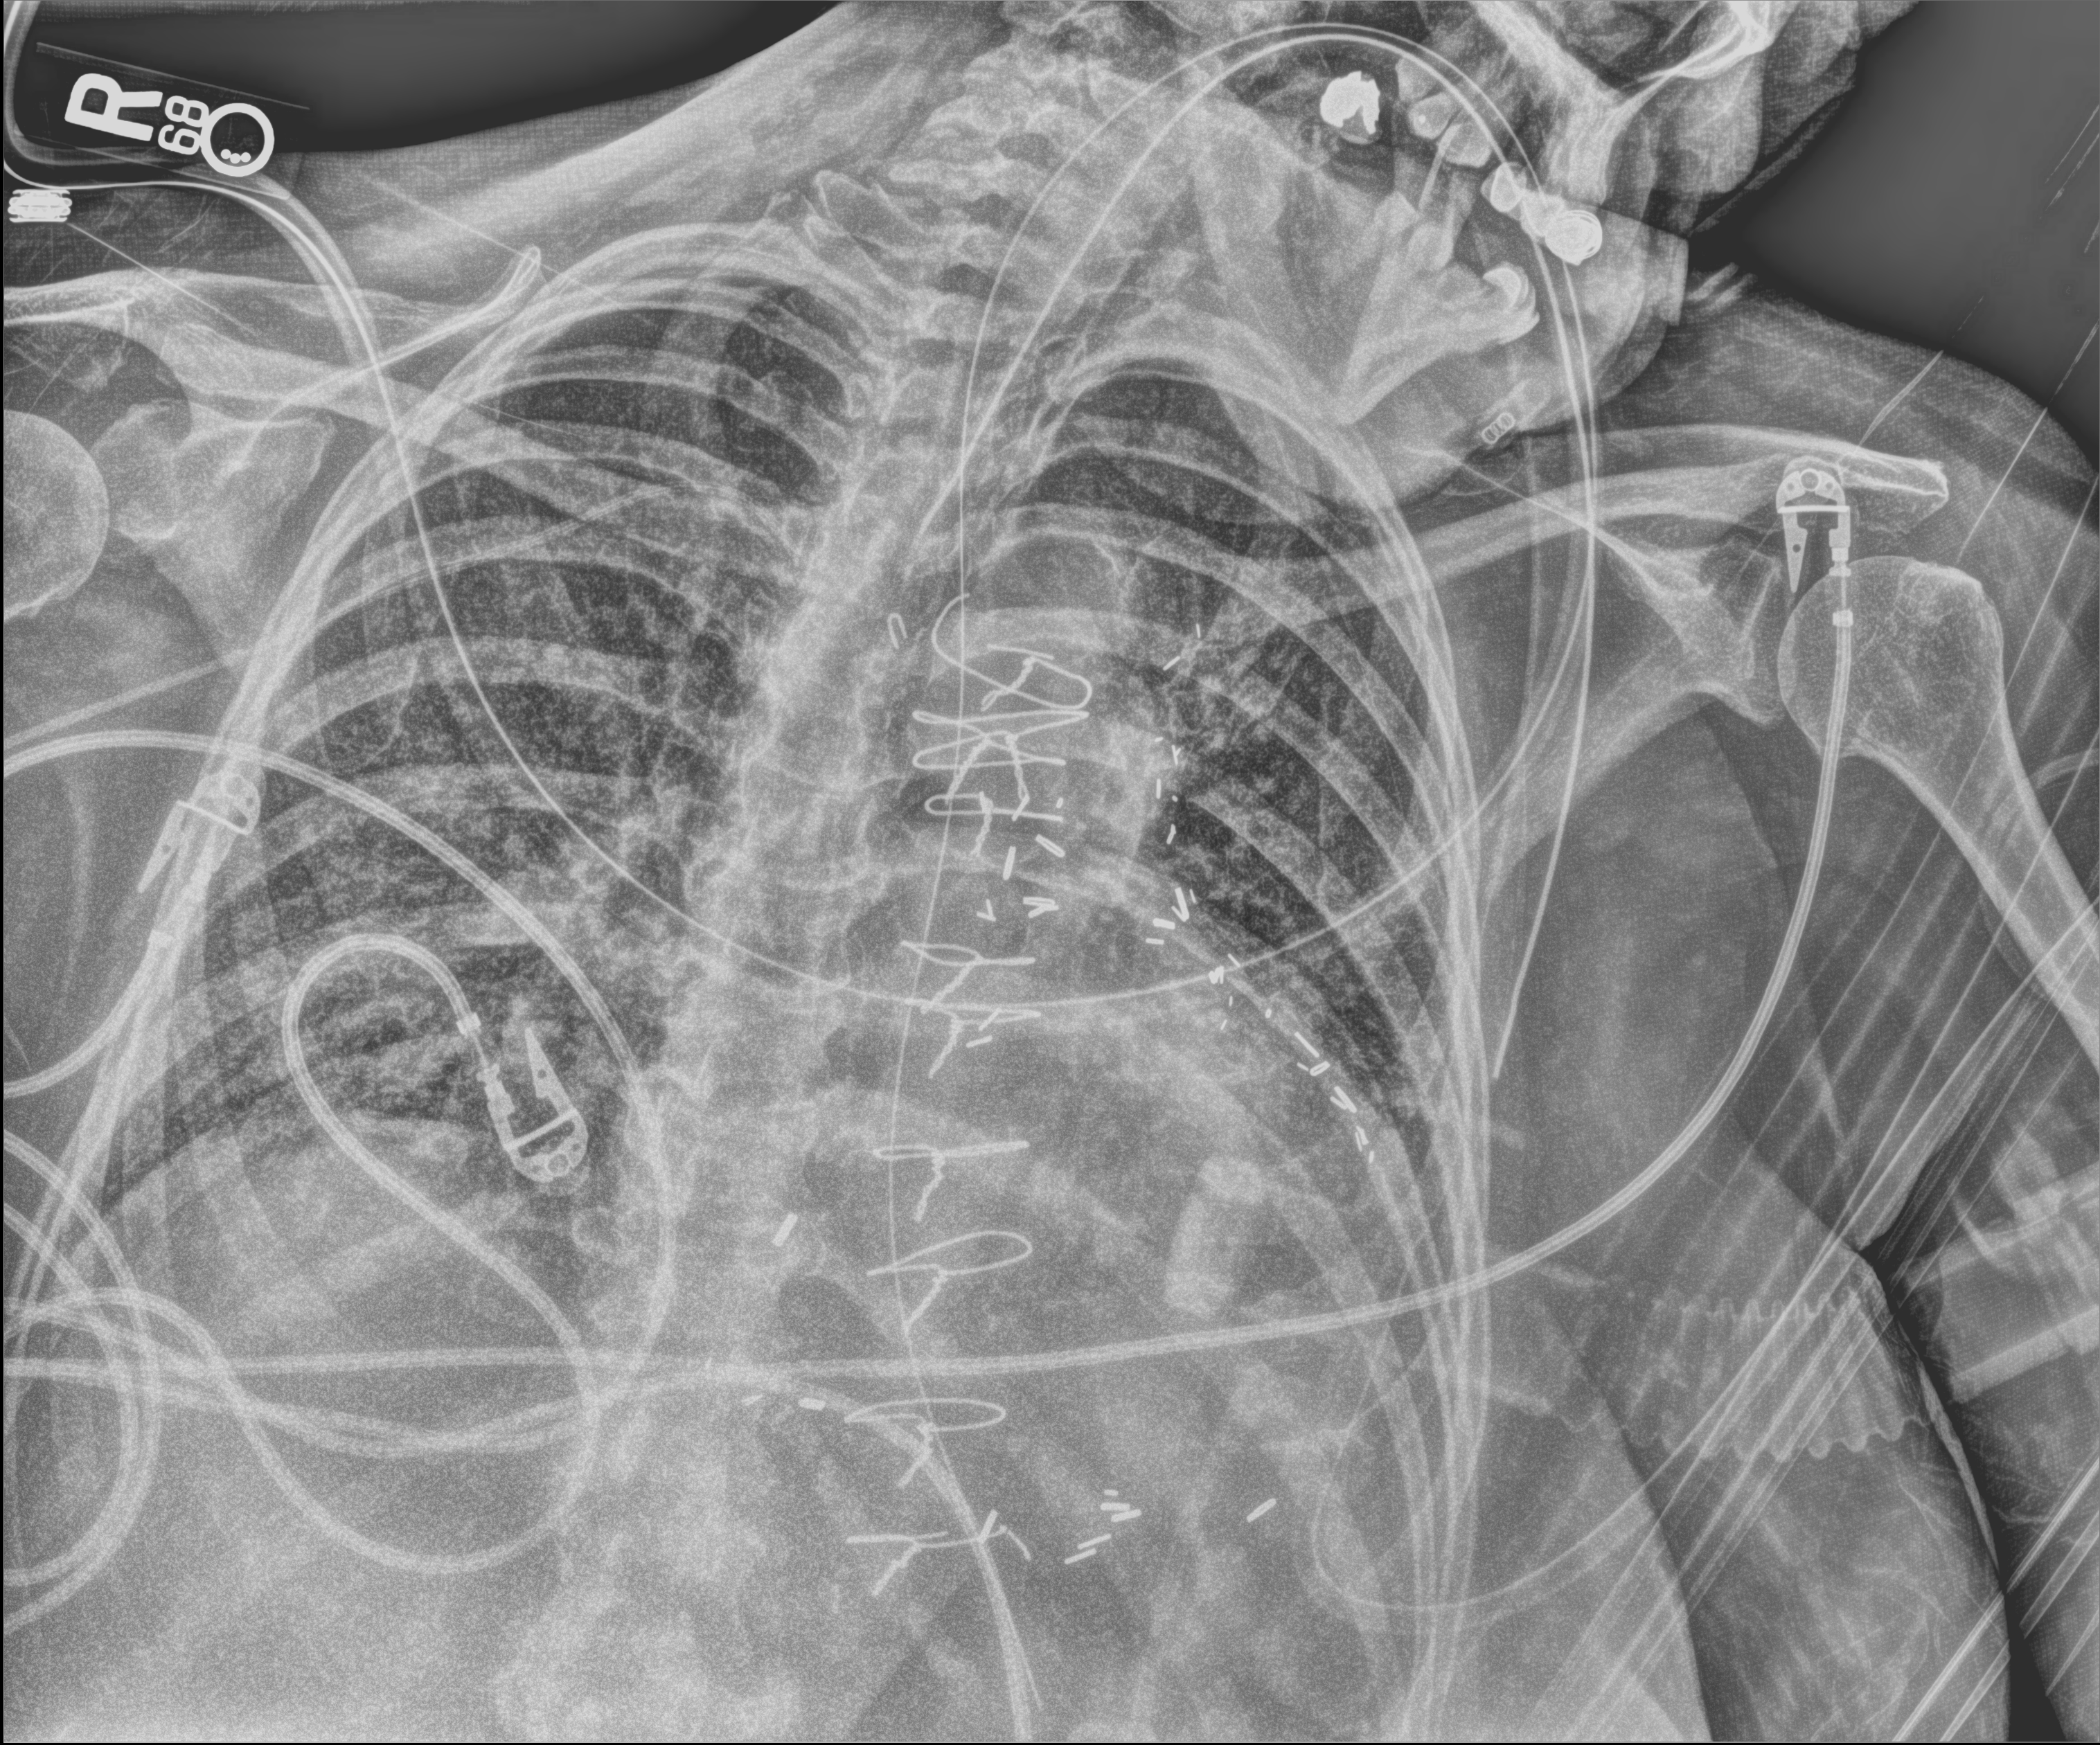
Bedside chest radiograph (digital radiography). Patient hospitalised with COVID-19; female, aged 60–74 years.
Hospital-stay facts (about this admission, not read from this image; timing relative to this image not recorded): hypertension (admission record): yes.